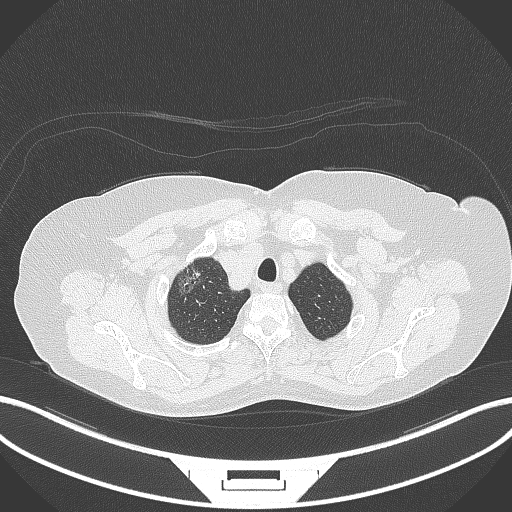
Chest CT, one axial slice; slice 313 of 365 in the series (ordered by position); lung window (W 1500 / L -600 HU); 1 mm slice thickness; 512 × 512 image matrix. Female patient, age 62 years. From the clinical record (not read from this slice): clinical TNM (as recorded): T1c N0 M0.
Structures marked on this image (bounding box drawn by a radiologist):
- lung tumour (recorded histology: adenocarcinoma): box from (x=176, y=257) to (x=206, y=298) px